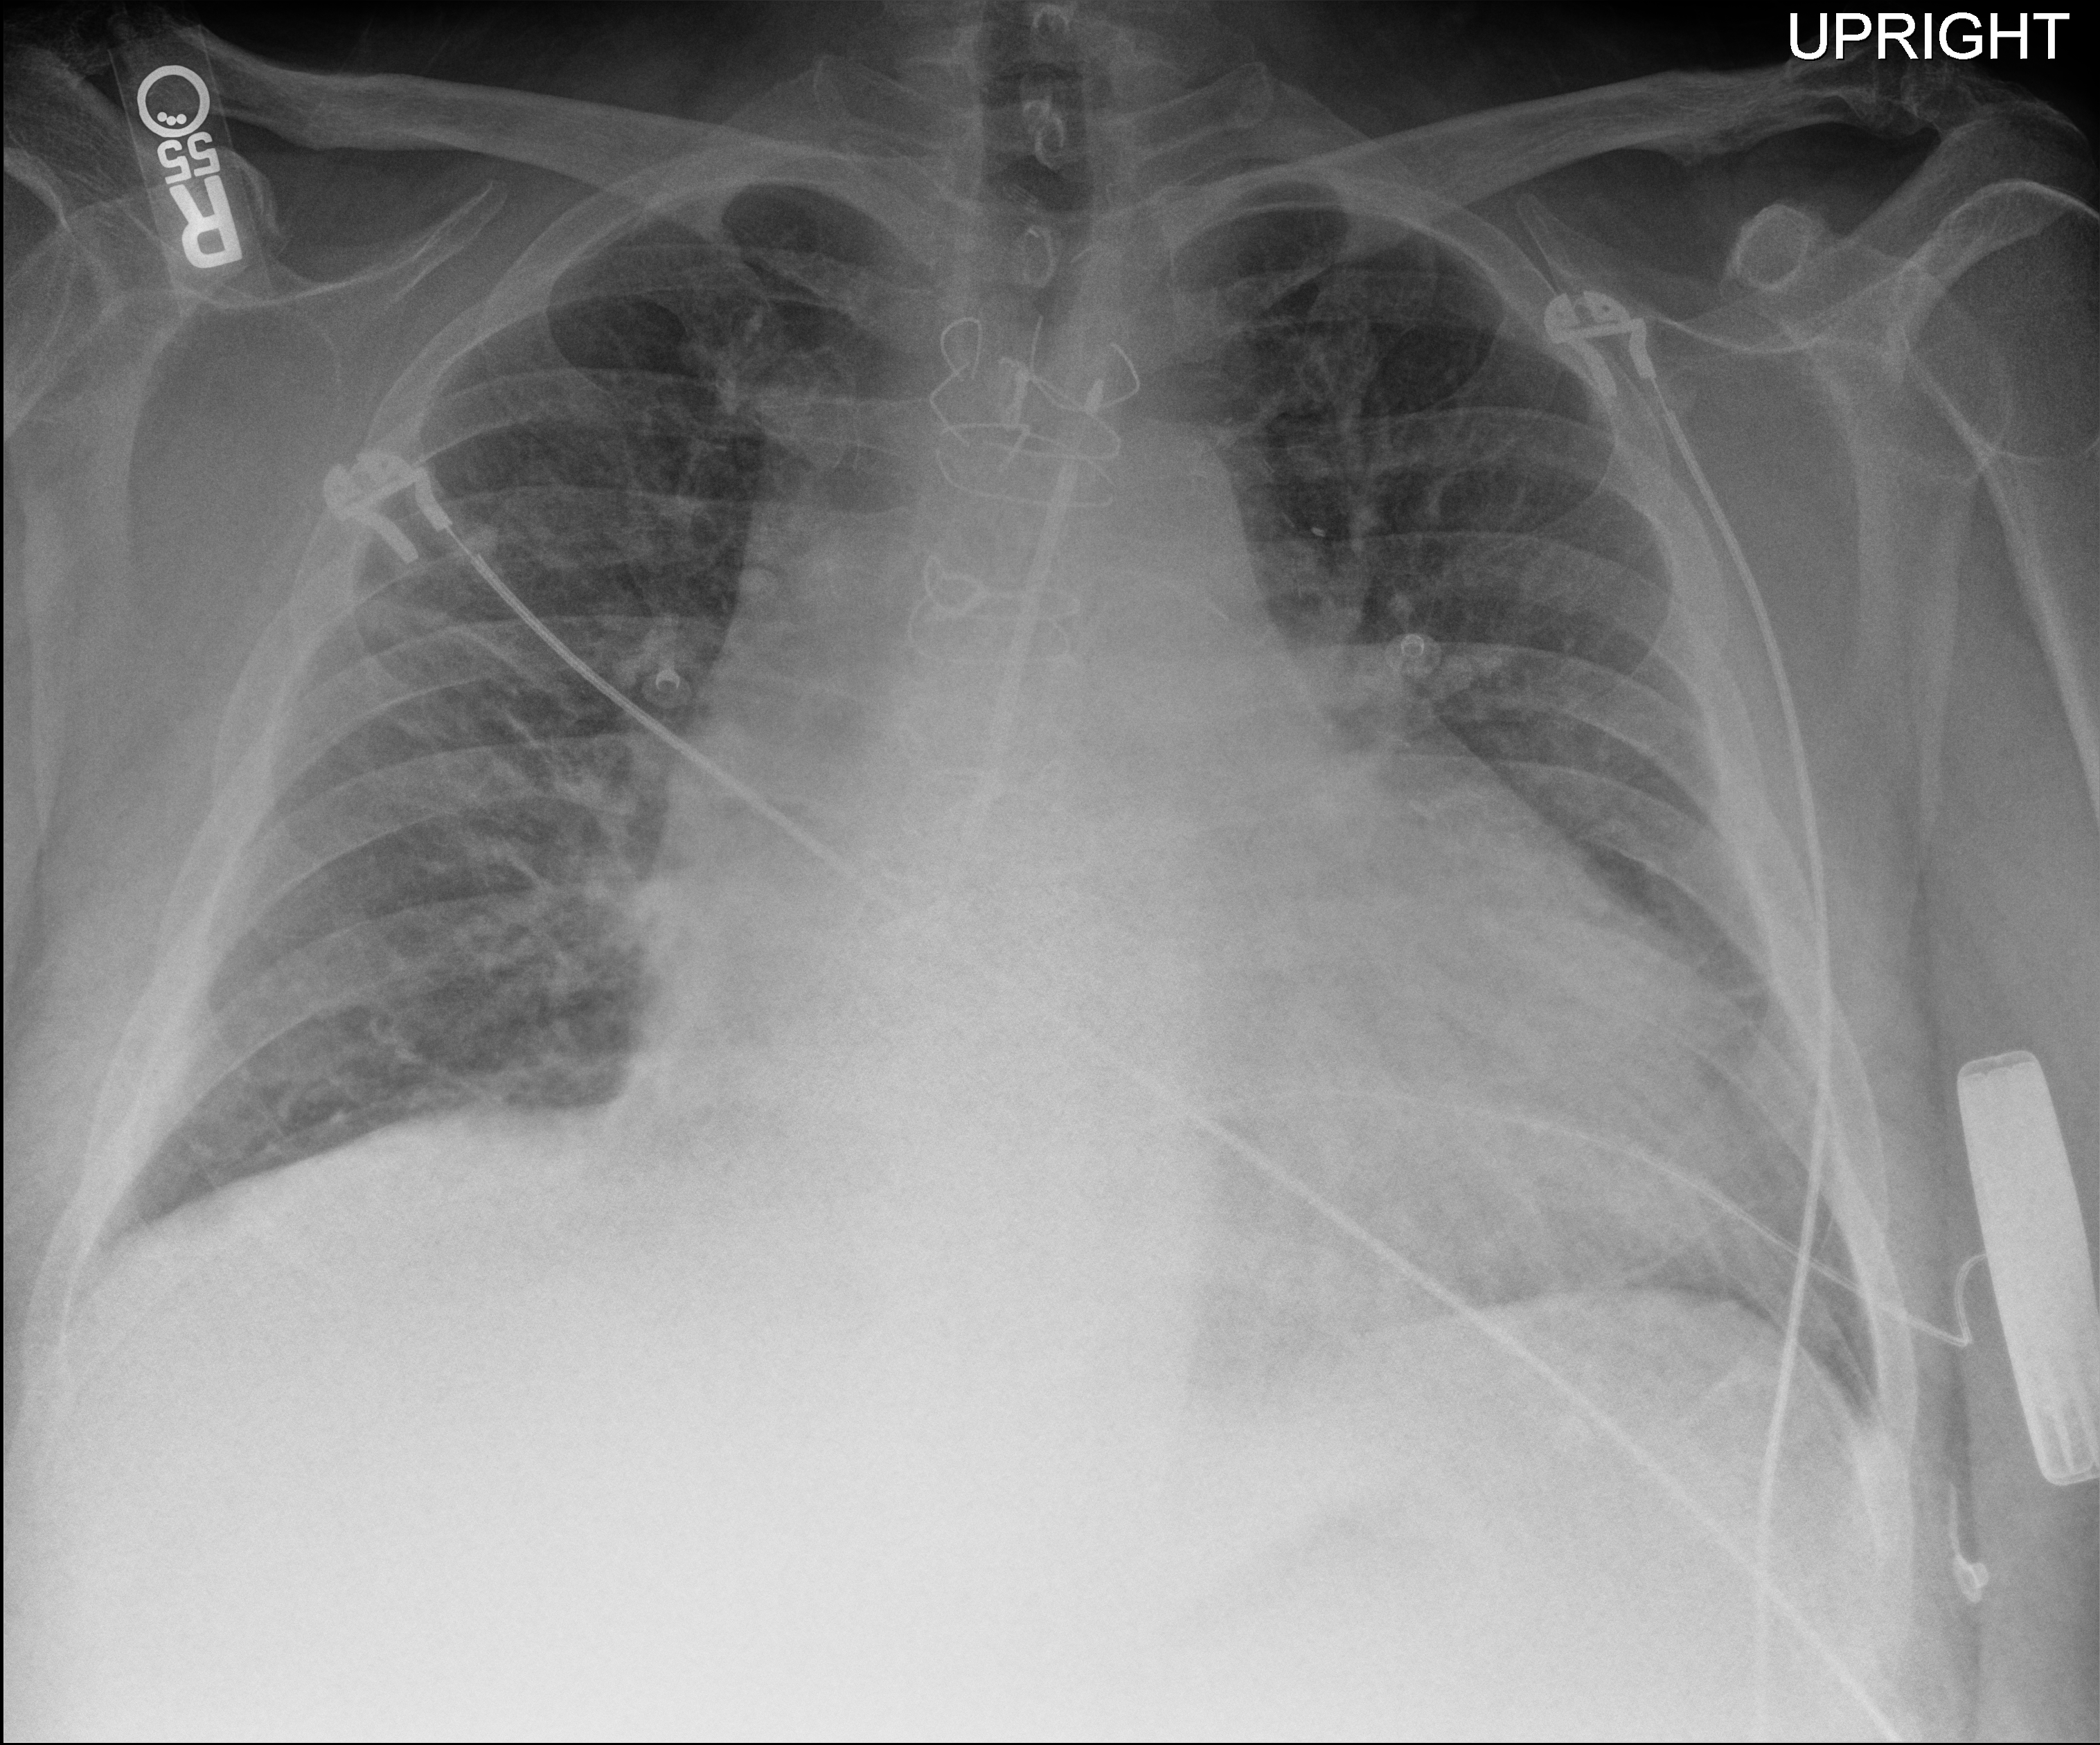
Chest radiograph (digital radiography); anteroposterior (AP) projection. Male patient hospitalised with COVID-19, age 60–74 years.
Hospital-stay facts (about this admission, not read from this image; timing relative to this image not recorded): length of hospital stay: 10 days; admitted to intensive care during this hospital stay: no.